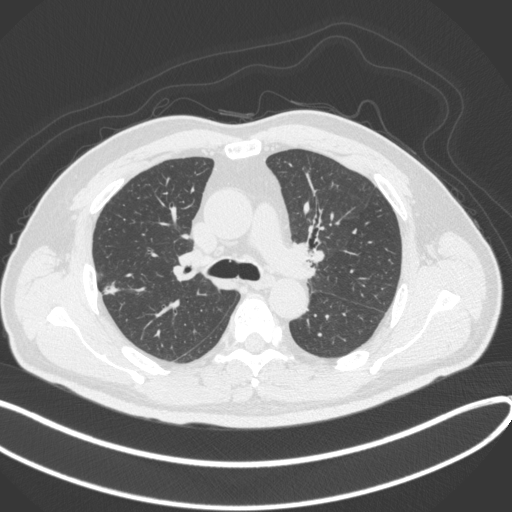
Chest CT, one axial slice. Position 223 of 373 along the scan axis. Reconstruction kernel B31f. Lung window (W 1500 / L -600 HU). 1 mm slice thickness. 512 × 512 image matrix. Male patient, age 60 years. Case-level facts recorded for this patient, not image findings: clinical TNM (as recorded): T1c N0 M0.
Annotated regions visible in this slice (bounding box drawn by a radiologist):
- lung tumour (recorded histology: adenocarcinoma): bounding box <101,280,126,303> (left, top, right, bottom; pixels)